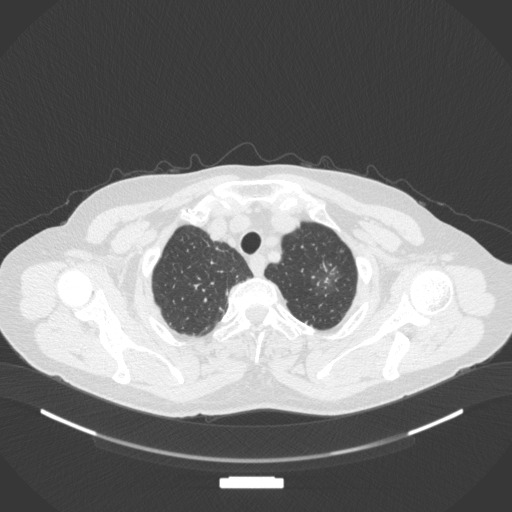
Chest CT, one axial slice; slice 317 of 369 in the series (ordered by position); 120 kVp; lung window (W 1500 / L -600 HU); 1 mm slice thickness; 512 × 512 image matrix, field of view 400 × 400 mm. Female patient, age 64 years. From the clinical record (not read from this slice): clinical TNM (as recorded): T1c N0 M0.
Structures marked on this image (bounding box drawn by a radiologist):
- lung tumour (recorded histology: adenocarcinoma): bounding box [x1, y1, x2, y2] px = [314, 256, 341, 291]